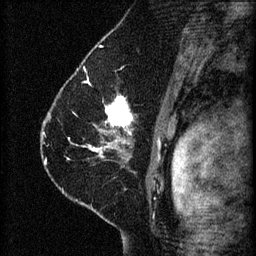
Breast MRI (dynamic contrast-enhanced), one sagittal slice. Position 42 of 60 along the scan axis. 3 images stored at this slice position (order not interpretable as contrast timing). 1.5 T. TE 4.2 ms, TR 8.2 ms. 256 × 256 image matrix. Patient: female, 41 years.
Structures marked on this image (semi-automatically segmented with operator editing):
- analysis volume of interest (the breast-tissue region the enhancement analysis was run in; not a lesion): box from (x=67, y=92) to (x=165, y=173) px
- tumour enhancement mask (voxels above the 70 % enhancement threshold inside the analysis volume of interest): (x=89, y=96)–(x=132, y=159)